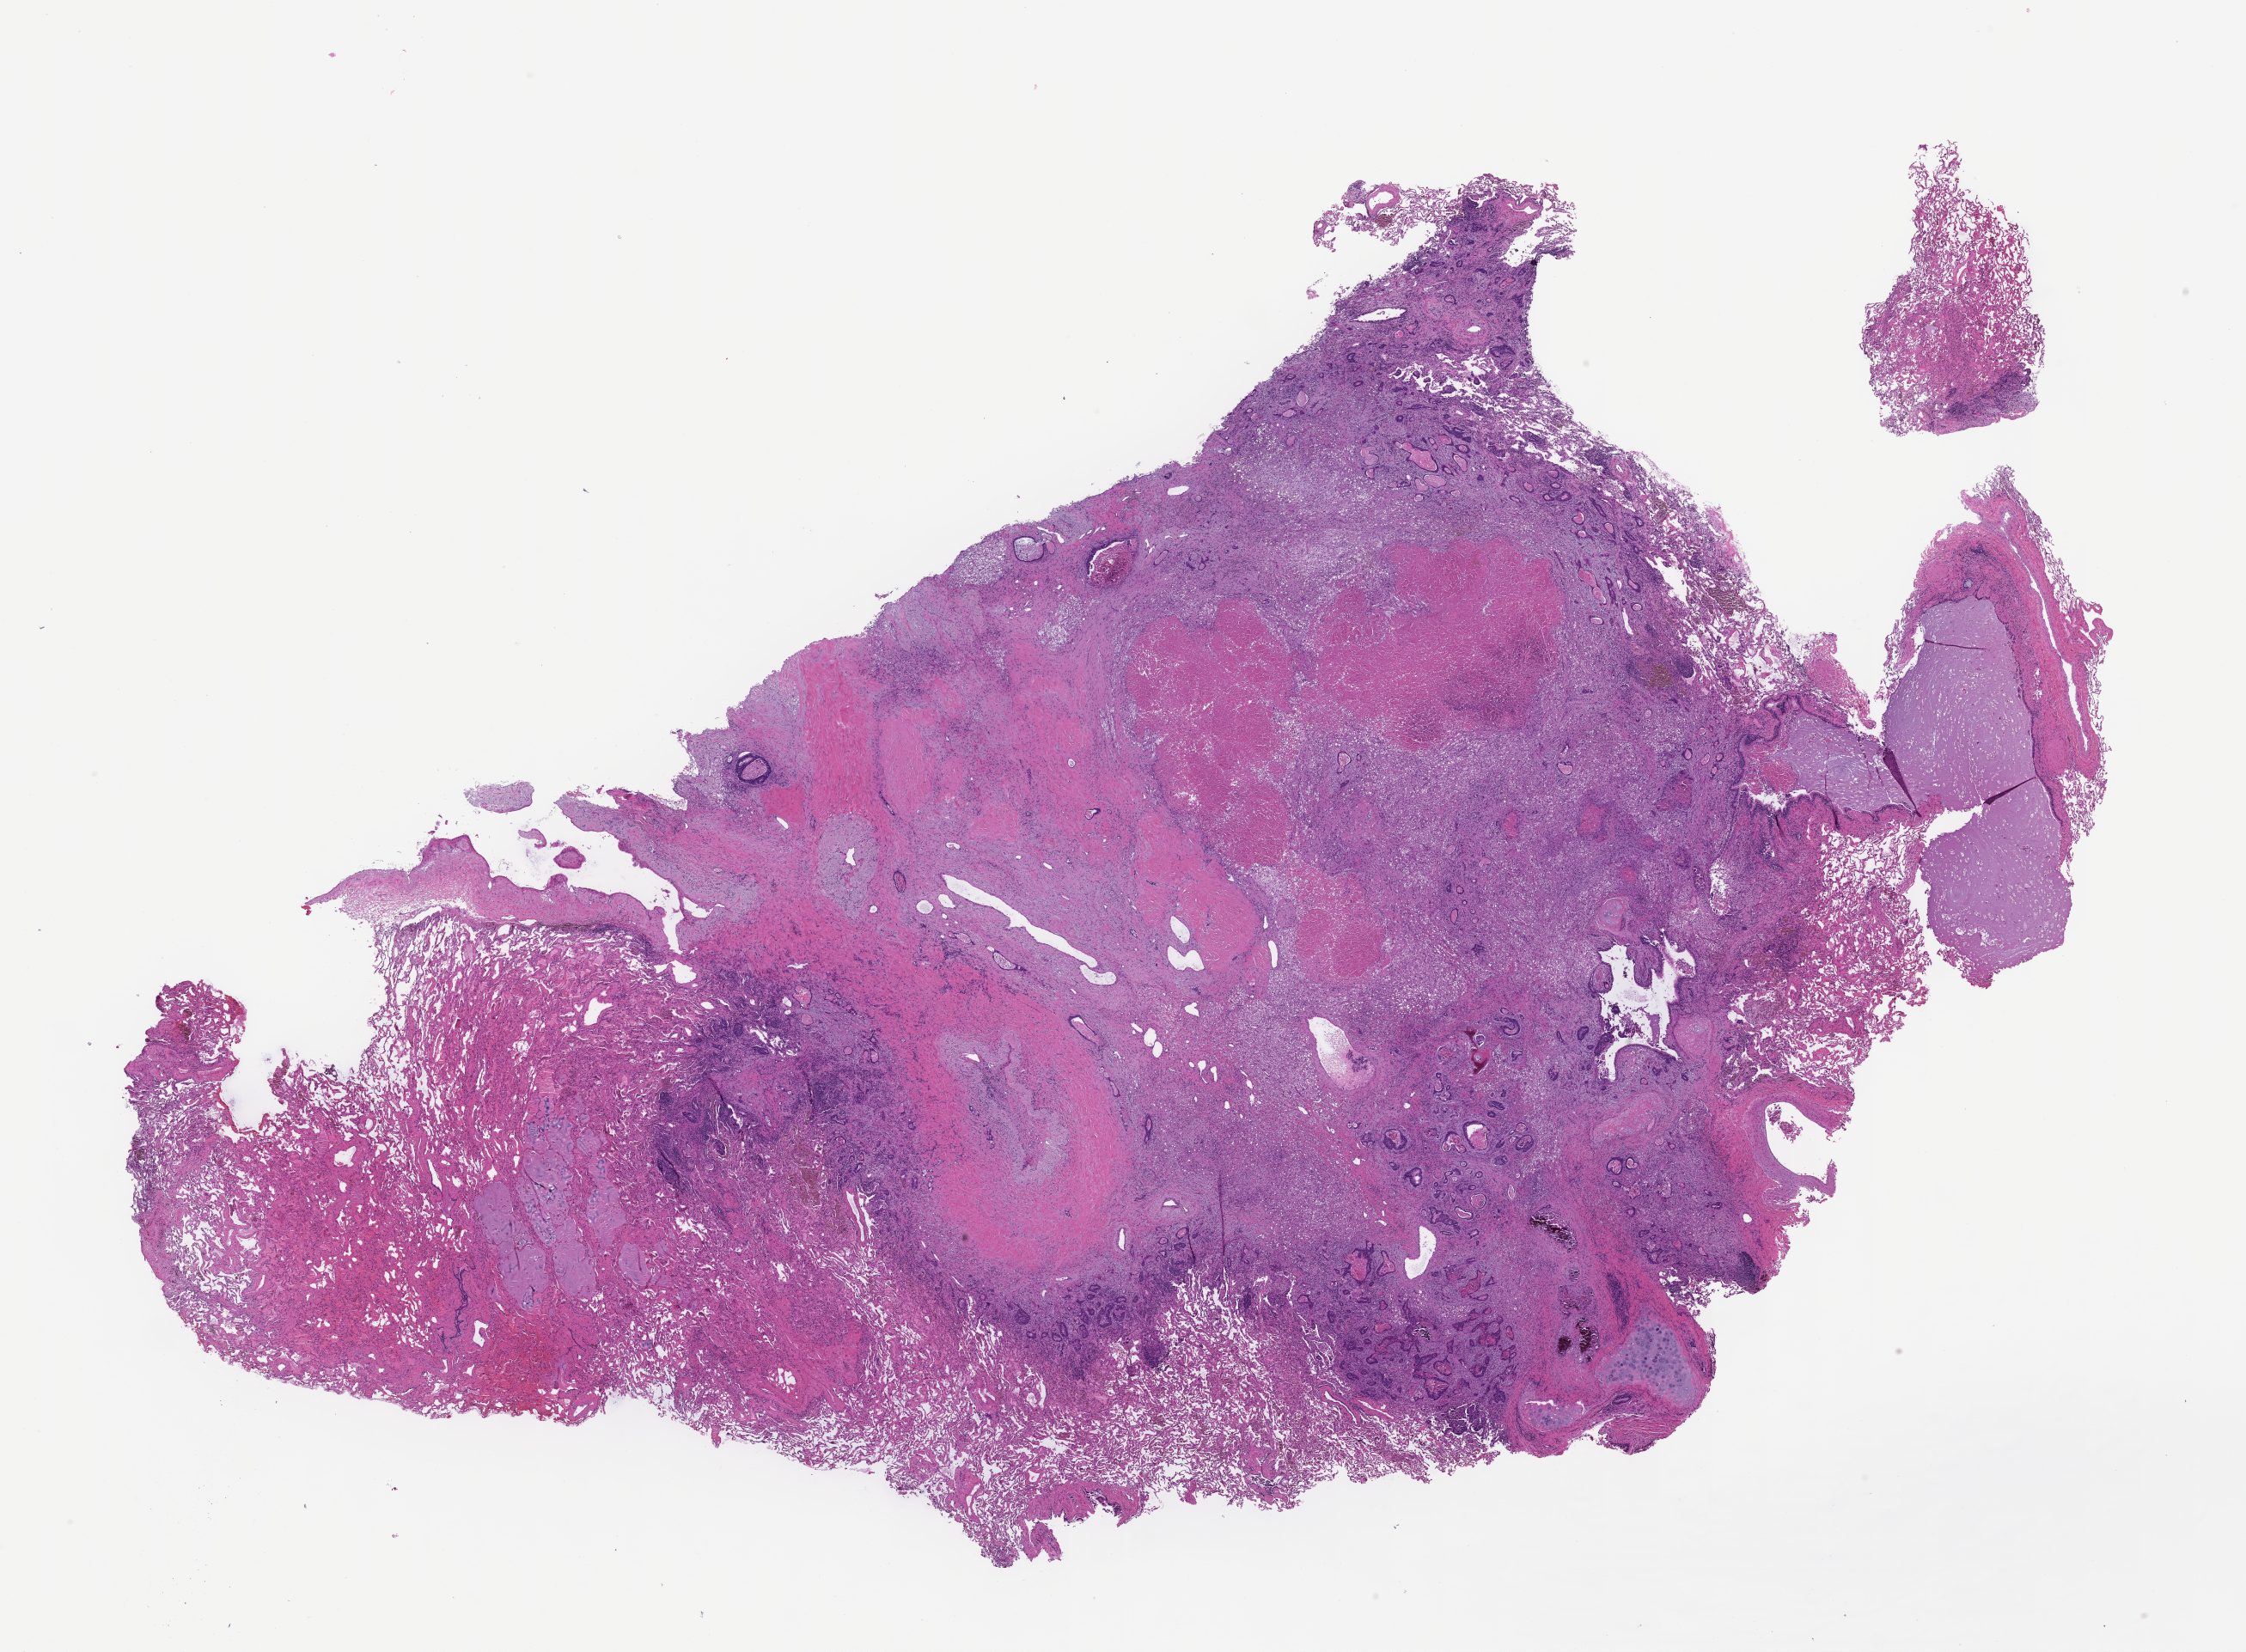
Whole-slide image, haematoxylin and eosin stain, shown as a low-resolution overview of the whole scanned area (about 21.1 x 15.5 mm), formalin-fixed paraffin-embedded section, specimen time point: collected on treatment. Male patient.
This section: metastasis (sampled organ not recorded). Patient diagnosis (primary): Colorectal Carcinoma.